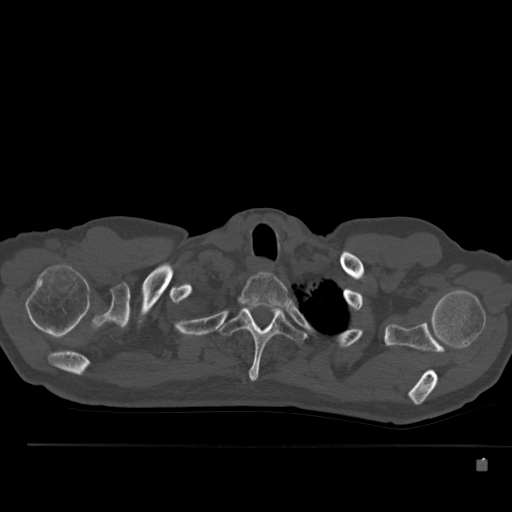
CT including the spine, one axial slice. Position 417 of 517 along the scan axis. 120 kVp. Bone window (W 1800 / L 400 HU). 1.5 mm slice thickness. 512 × 512 image matrix, field of view 408 × 408 mm. Patient: male, 70 years. Case-level facts recorded for this patient, not image findings: primary cancer: renal; vertebrae with lytic lesions (as recorded): T4, T6, T10, T12, L3, L4, L5.
Annotated regions visible in this slice (semi-automatically segmented with operator editing):
- T1 vertebra: bounding box (x1, y1, x2, y2) in pixels: (242, 272, 290, 307)
- T2 vertebra: (219, 305, 305, 382)